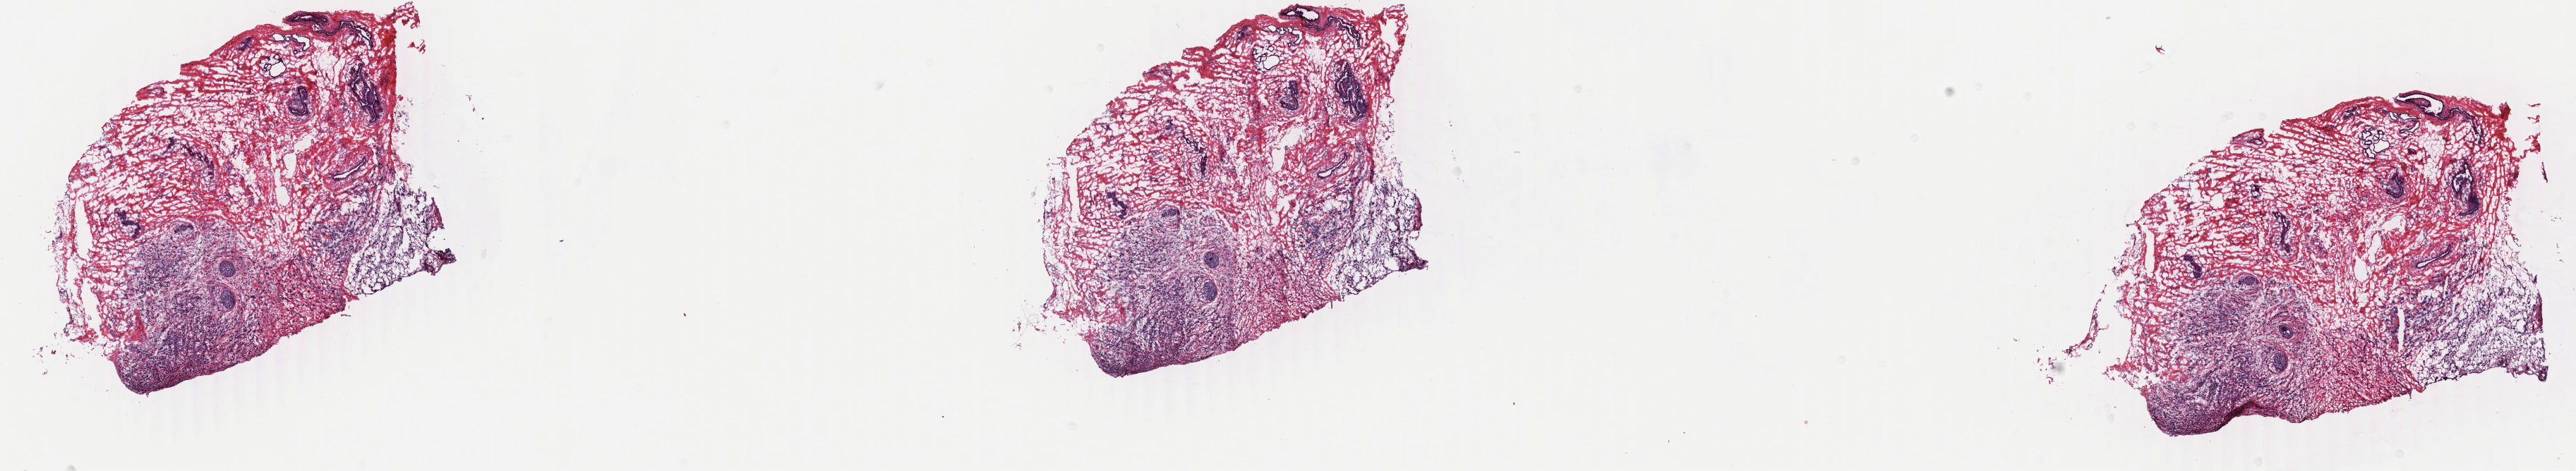
Whole-slide histology image, H&E, whole scanned area (about 29.0 x 5.3 mm) shown as a low-resolution overview; frozen section from the bottom of the tissue portion; primary tumour sample from the breast. Female patient; age at initial diagnosis 55 years. Slide review estimates, as recorded: tumour cells 35%, tumour nuclei 60%.
Diagnosis: Infiltrating duct carcinoma, NOS.